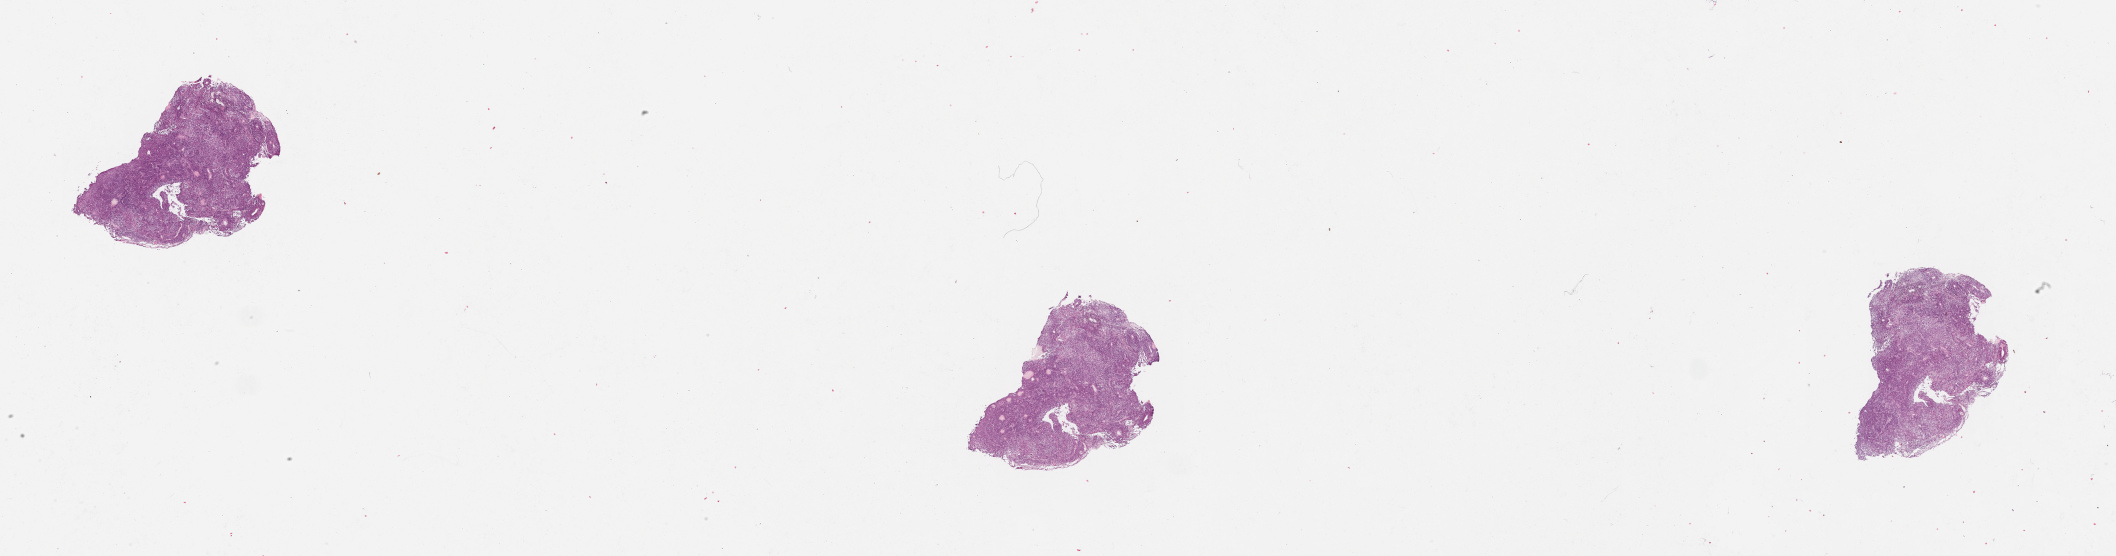
Whole-slide histology image, H&E — low-resolution overview of the scanned area, about 34.1 x 9.0 mm (from a 20x scan), tumour tissue sample, sampled site: uterus. Patient: female, age 68 years. Composition of this section per pathologist review: tumour nuclei 80%, necrosis 5%.
Histologic diagnosis: Endometrioid adenocarcinoma, NOS.